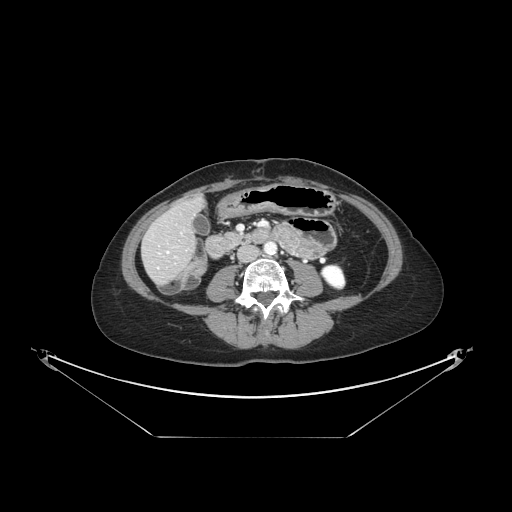
Contrast-enhanced abdominal CT, one axial slice; position 36 of 148 along the scan axis; reconstruction kernel STANDARD; intravenous contrast given; soft-tissue window (W 400 / L 40 HU); 2.5 mm slice thickness; 512 × 512 image matrix, field of view 500 × 500 mm. Female patient, age 73 years. From the clinical record (not read from this slice): diagnosis: colorectal cancer liver metastases, imaged before liver resection; multiple liver metastases: no; largest metastasis: 1 cm; disease in both lobes: no.
Outlined on this slice (outlined manually by an expert reader):
- liver: bounding box (x1, y1, x2, y2) in pixels: (143, 200, 202, 283)
- planned liver remnant (the part of the liver to remain after resection): (162, 200, 202, 240)